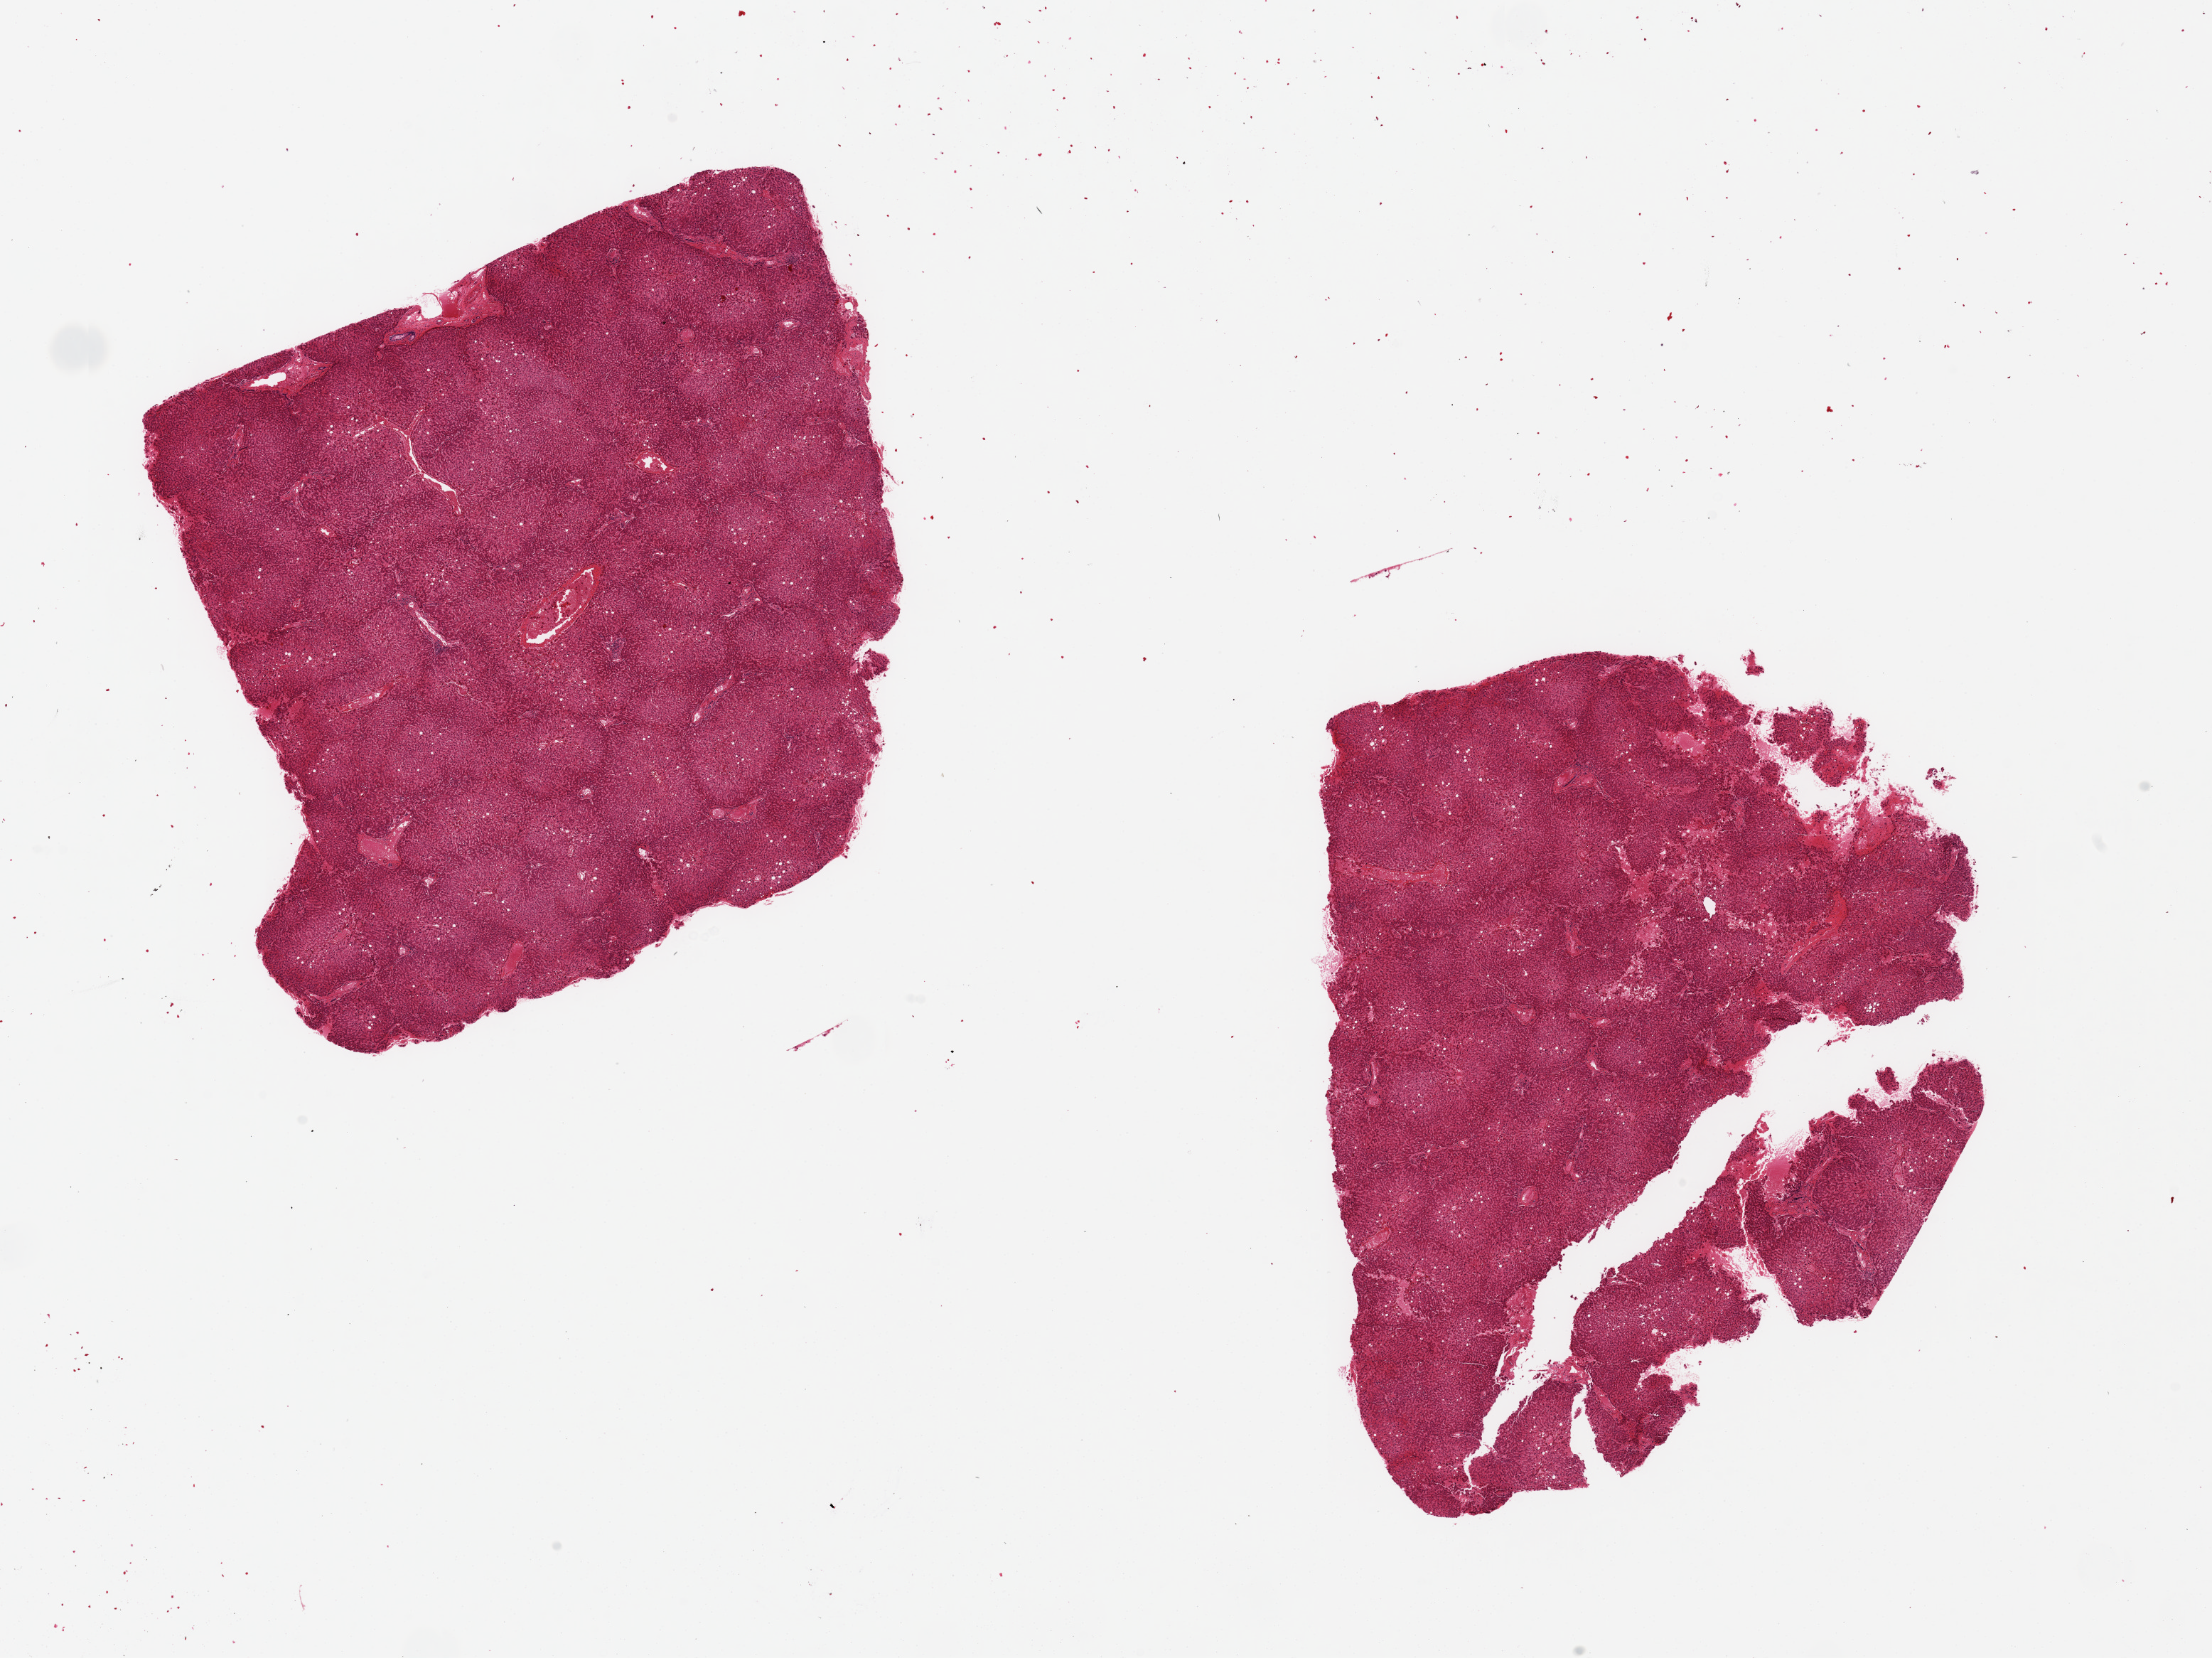
Digitized hematoxylin and eosin (H&E)-stained section, brightfield, whole scanned area (about 24.6 x 18.4 mm) shown as a low-resolution overview. PAXgene-fixed, paraffin-embedded tissue. Sampled site (target tissue): liver. Donor tissue sample. Male donor.
Reviewer comment on this tissue sample: 2 pieces ~ ~8x8mm. Chronic passive congestion, mild-moderate, minimal (<10%) macrovesicular steatosis.